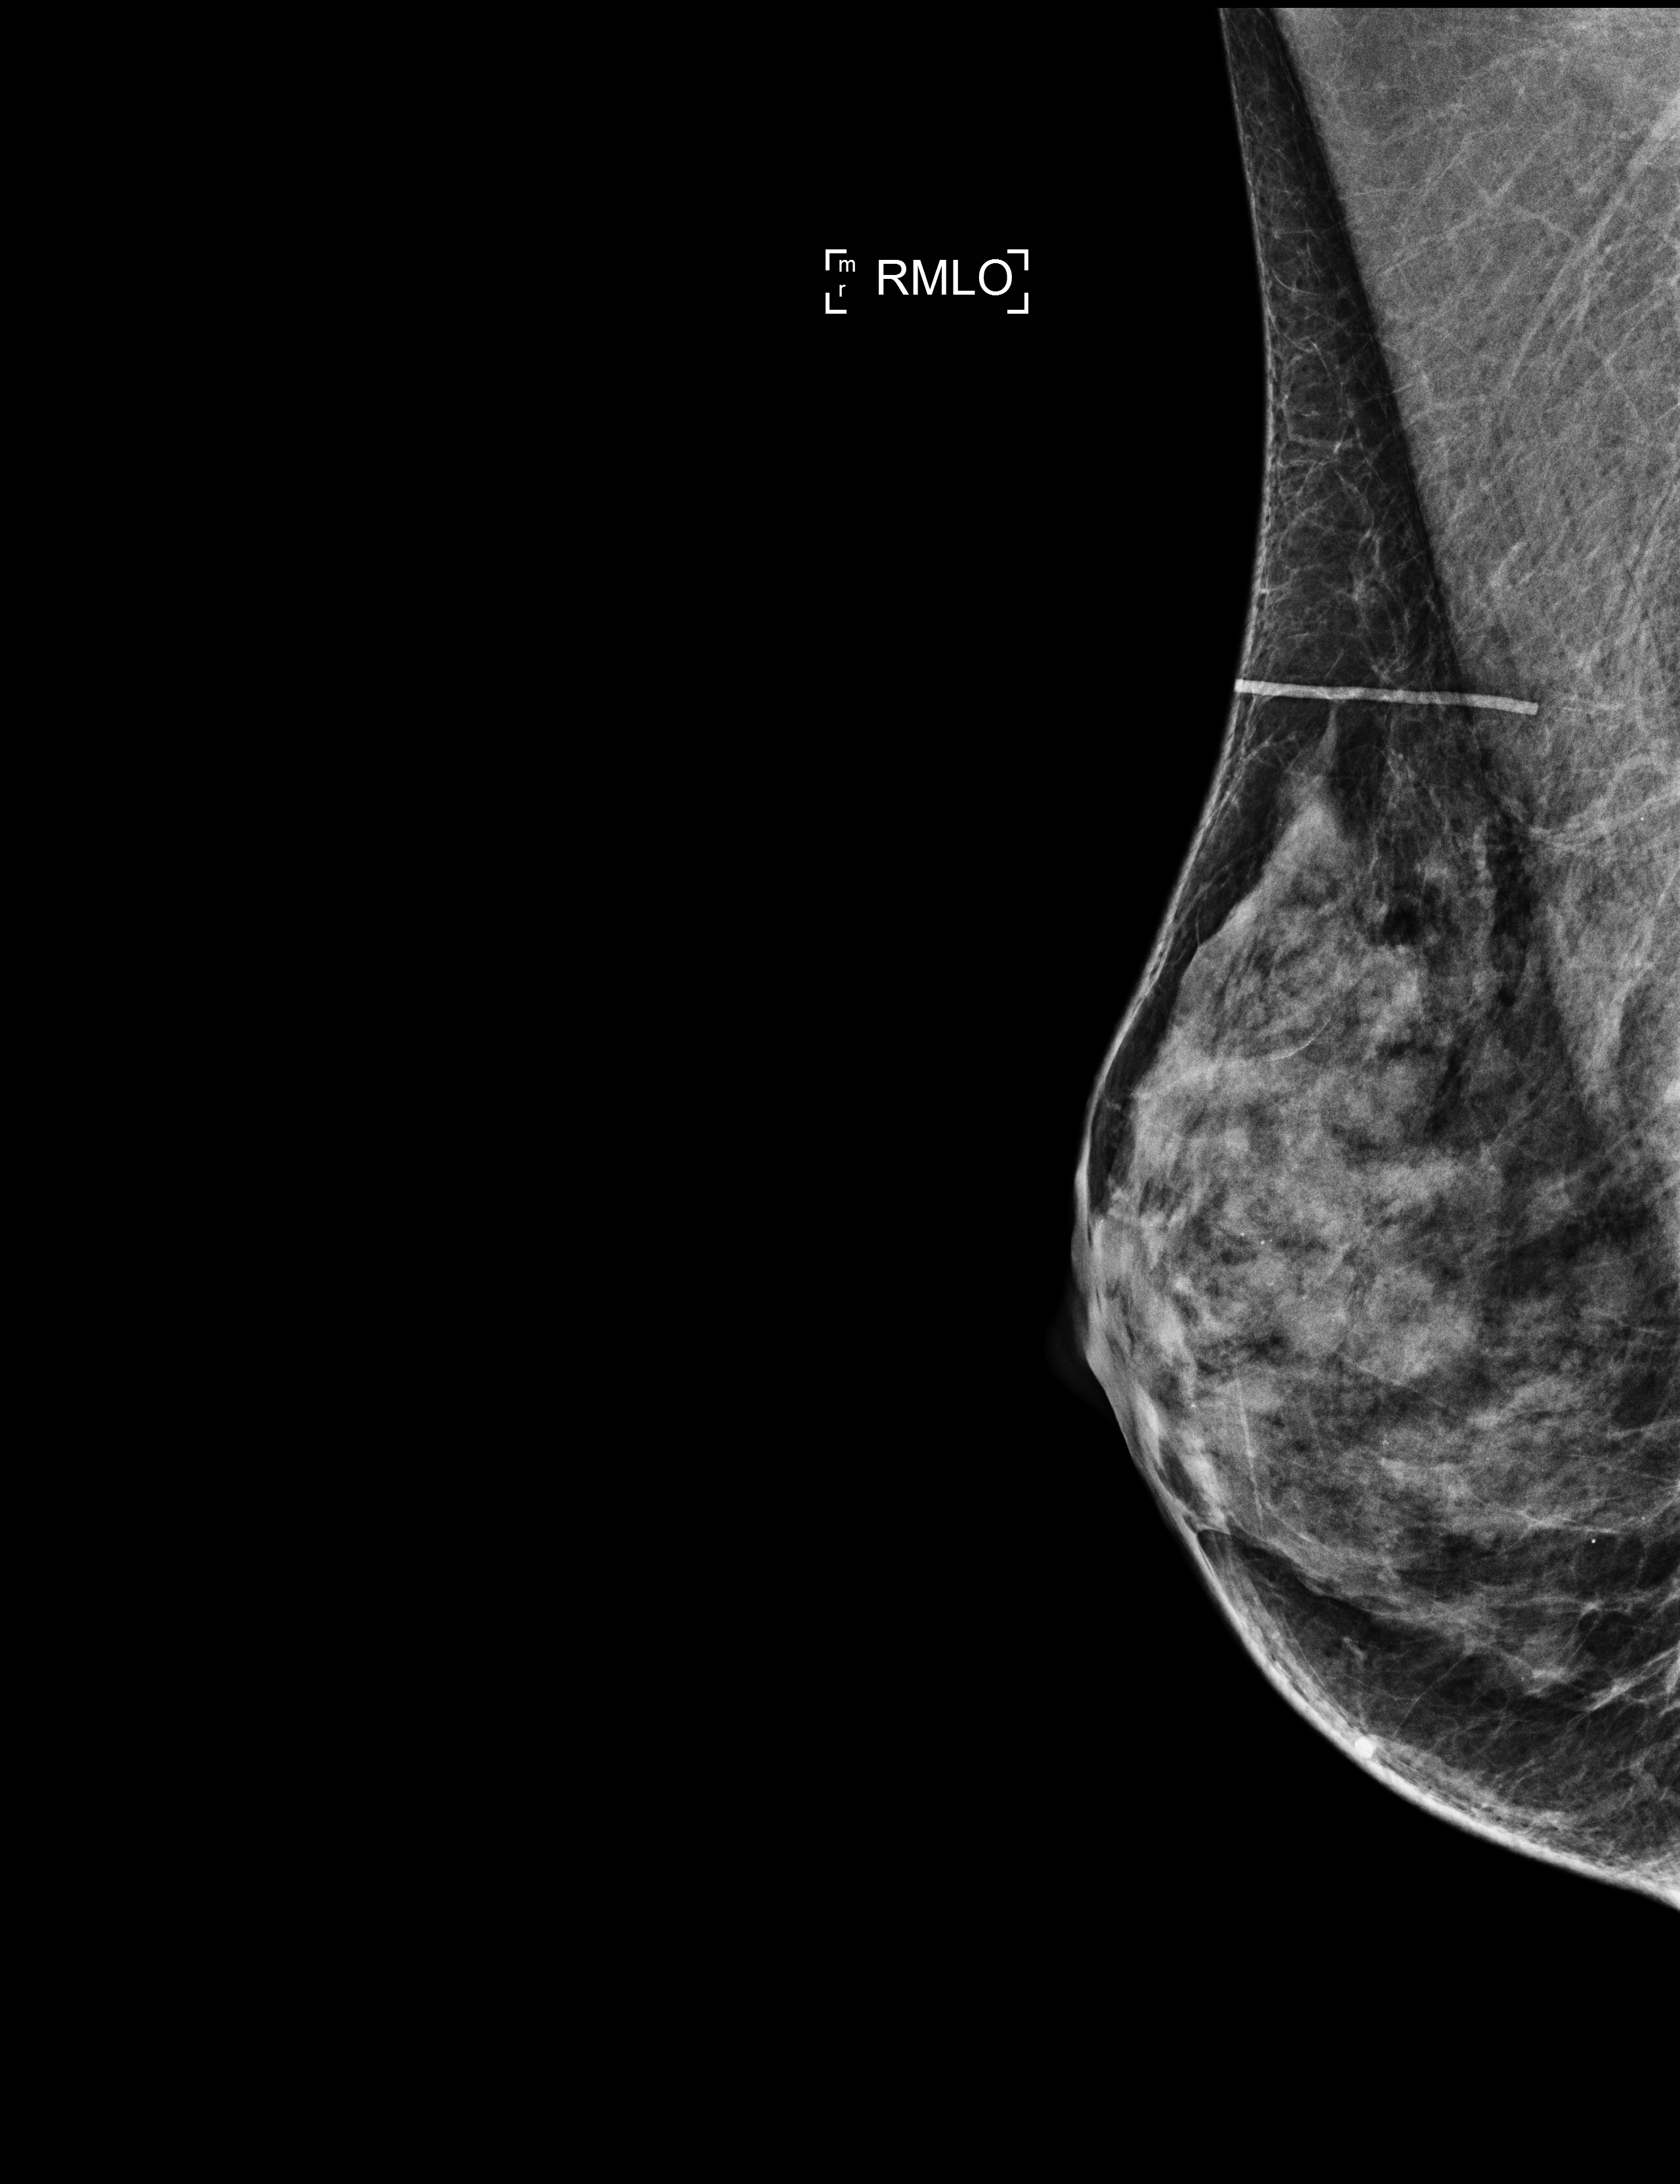
Annual screening mammography examination, compressed breast thickness 34 mm. Patient aged 51 years (female).
Image type: full-field digital mammogram. Breast: right. Projection: medio-lateral oblique projection.